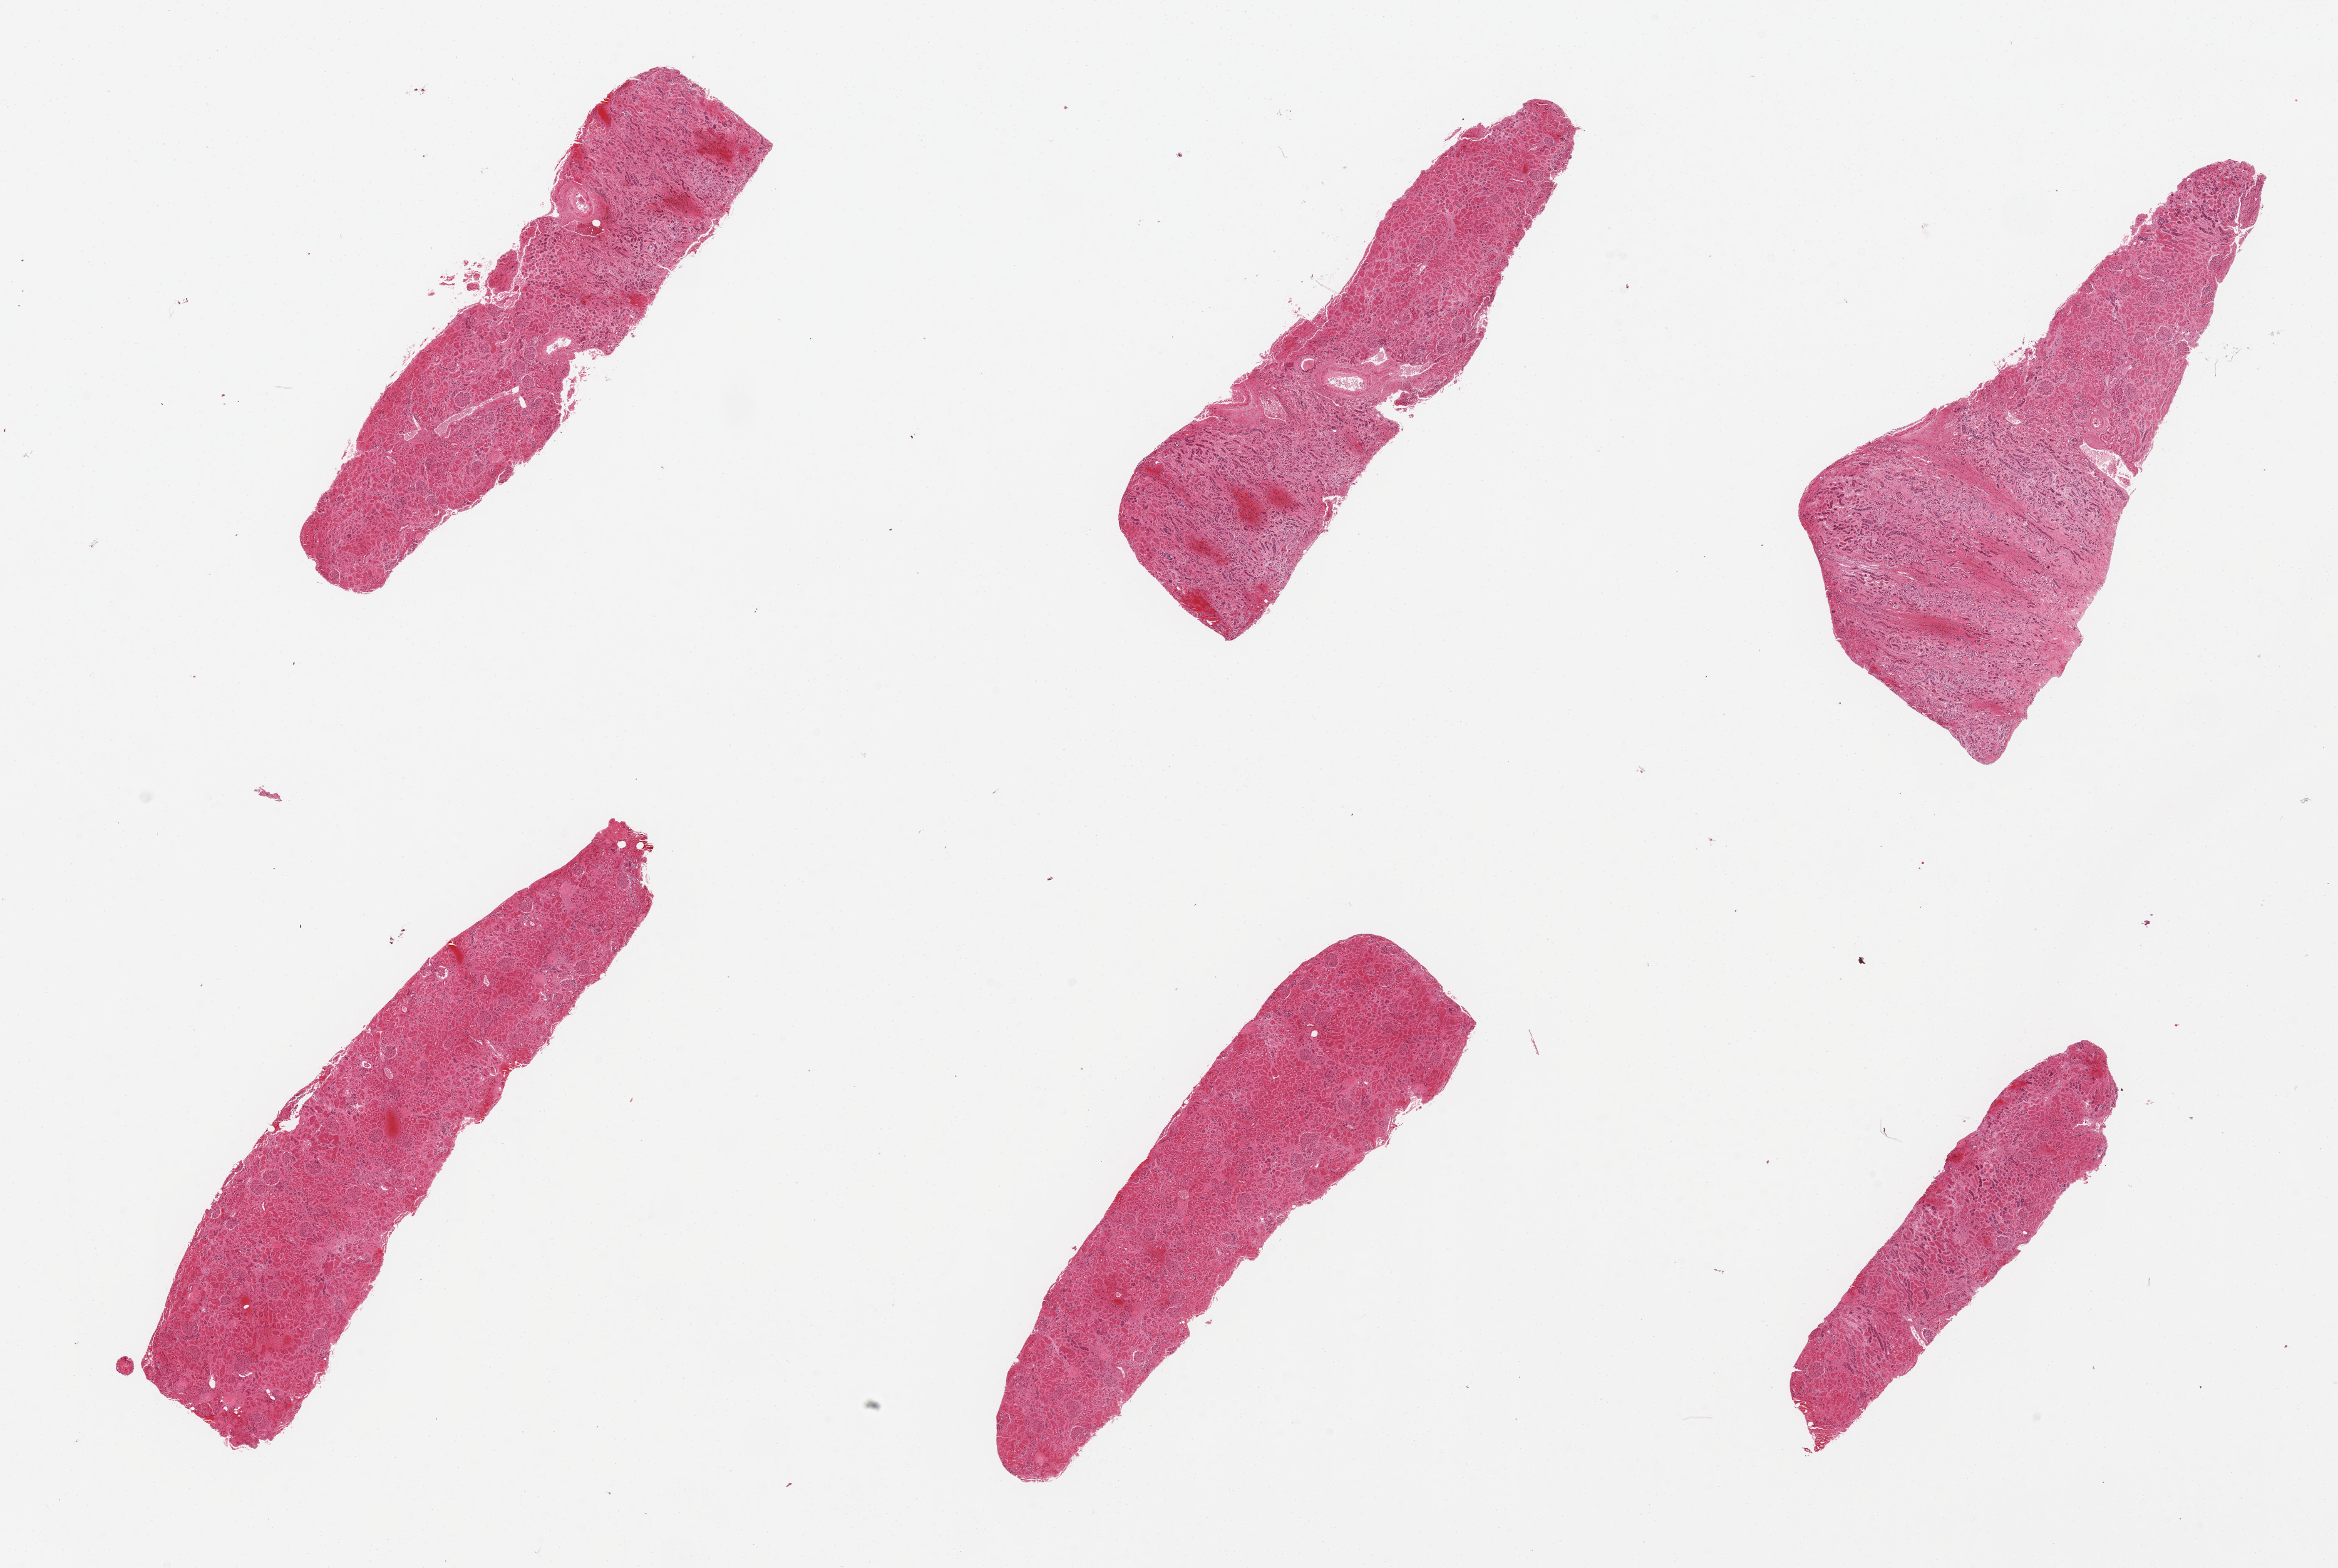
Digitized haematoxylin and eosin-stained section, brightfield — a low-resolution overview of the entire scanned area, about 29.5 x 19.8 mm, PAXgene-fixed, paraffin-embedded tissue, sampled site (target tissue): renal cortex, donor tissue sample. Donor: female.
Review note (as recorded): 6 pieces, glomeruli present, all badly autolyzed.